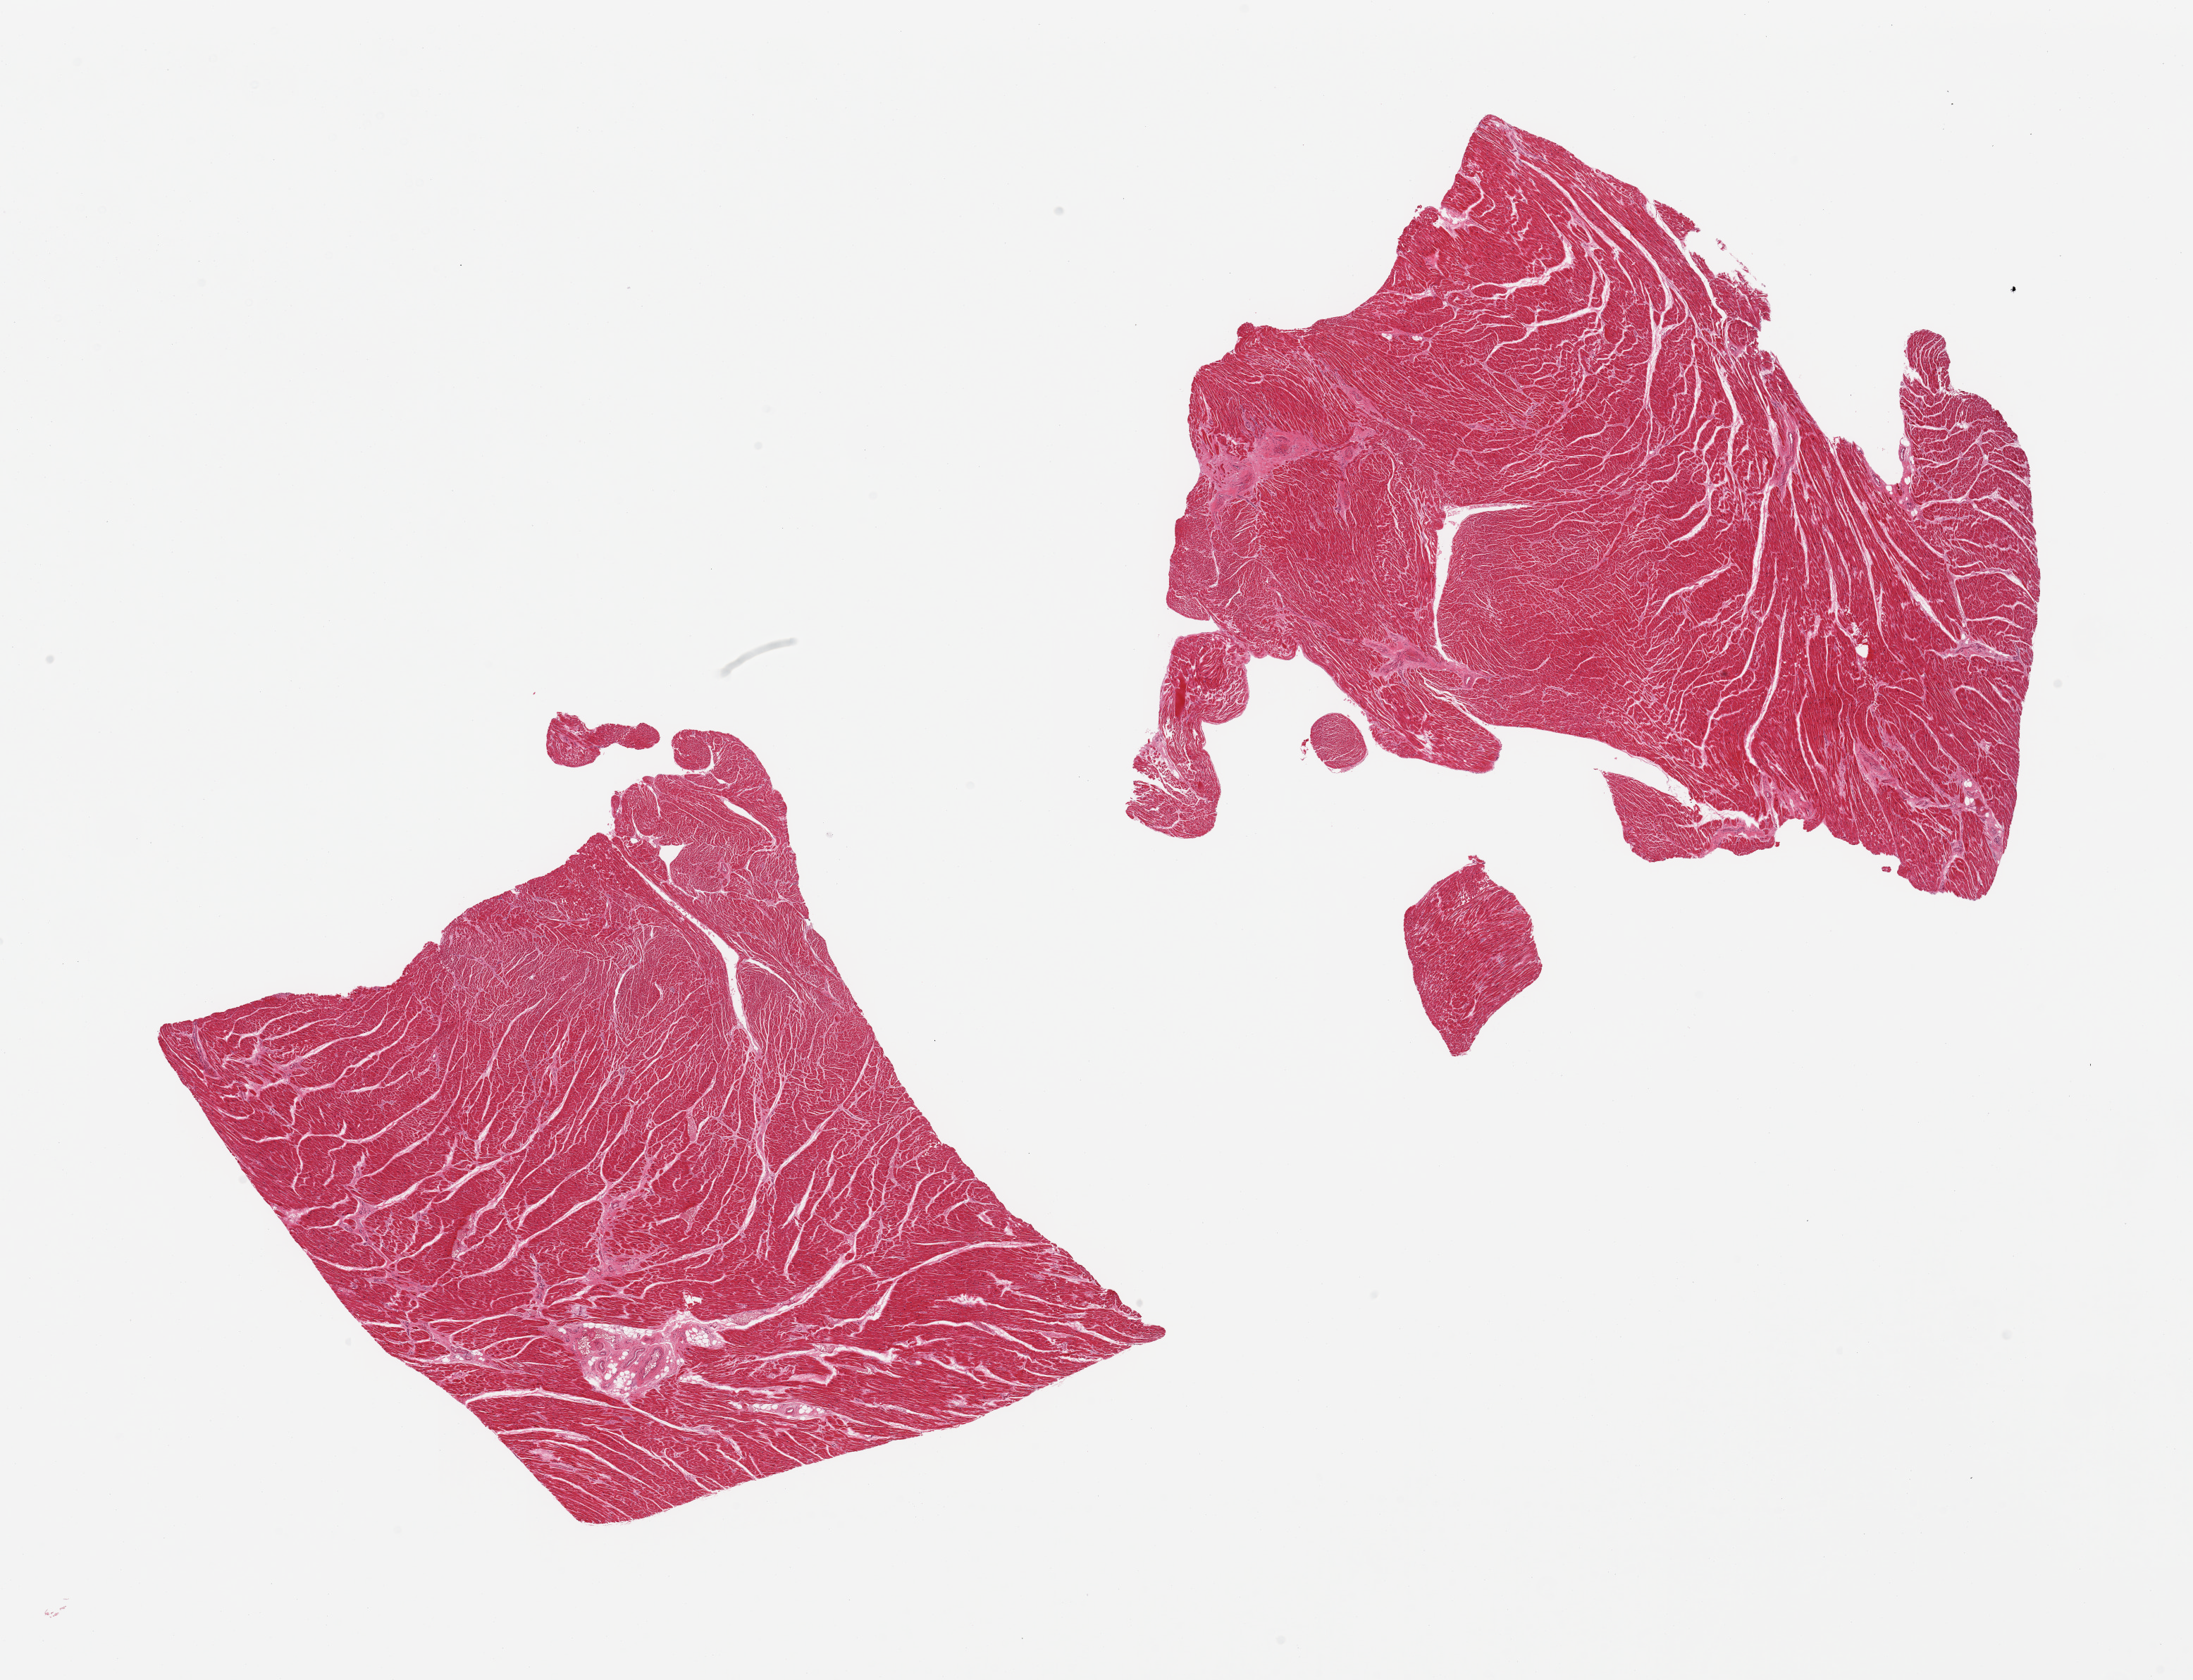
Whole-slide image, haematoxylin and eosin stain, shown as a low-resolution overview of the whole scanned area (about 24.6 x 18.9 mm). PAXgene-fixed paraffin-embedded (PFPE) section. Target tissue: heart. Tissue donor sample.
Pathologist's review note for this sample: 2 pieces; small fibrous foci.